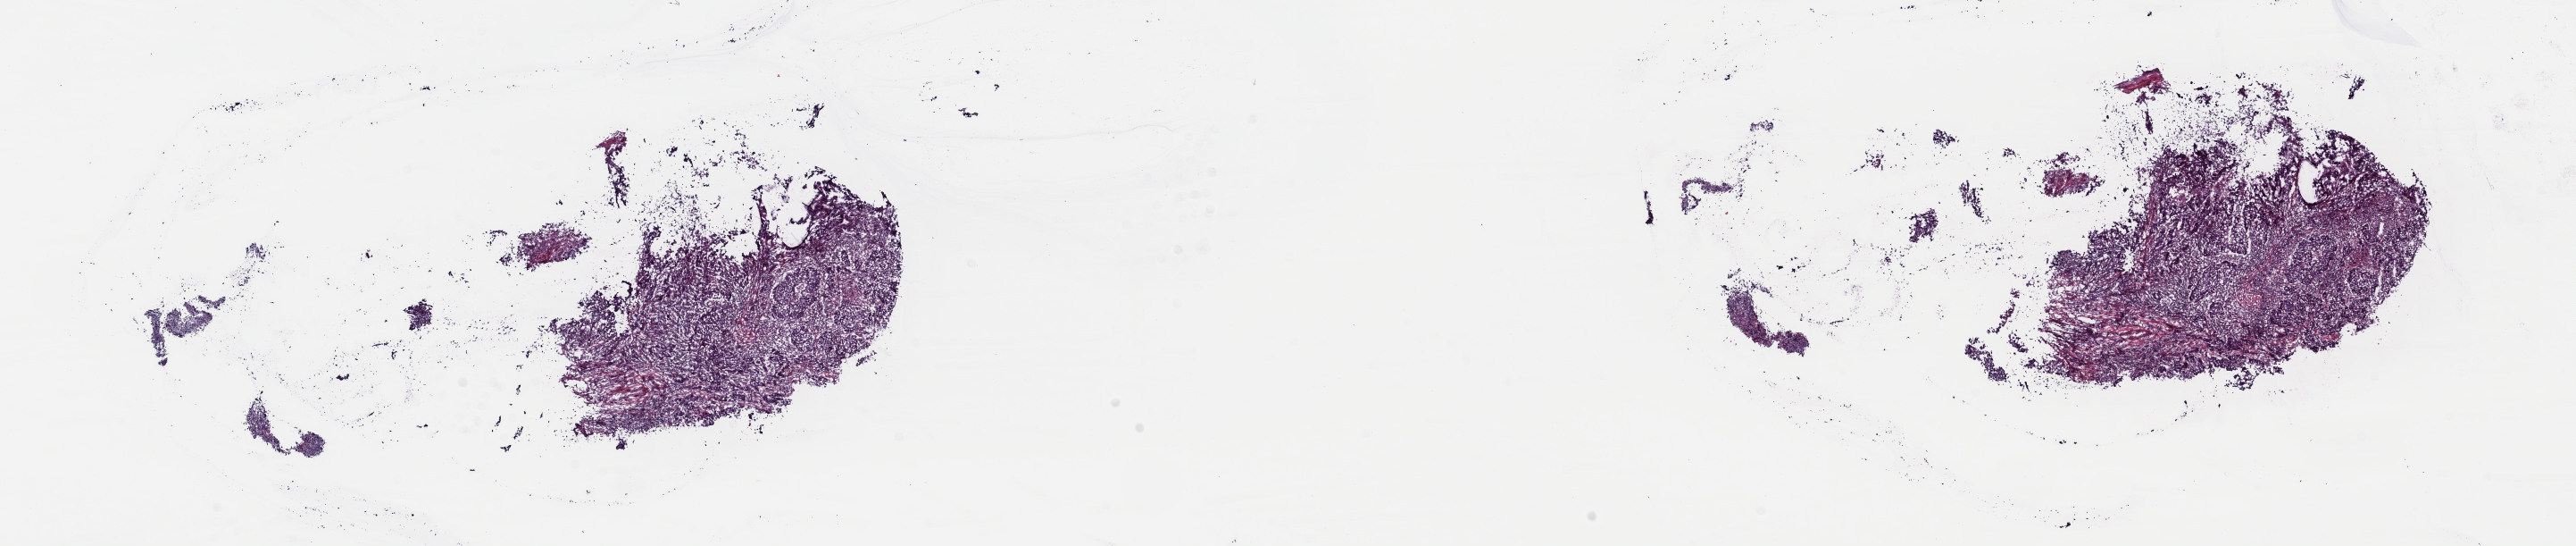
Hematoxylin and eosin (H&E) stained whole-slide image, a low-resolution overview of the entire scanned area, about 22.8 x 4.8 mm. Frozen section. Primary tumour sample from the lung. Patient: male, age at initial diagnosis 60 years. Slide review estimates, as recorded: tumour cells 60%, tumour nuclei 85%, normal cells 0%, stromal cells 35%, necrosis 5%. Inflammatory infiltration, as recorded: lymphocyte infiltration 20%, monocyte infiltration 5%, neutrophil infiltration 4%.
AJCC pathologic stage: IIB (6th edition). Laterality: left. Histologic diagnosis: Squamous cell carcinoma, NOS. TNM: T2 N1 M0.